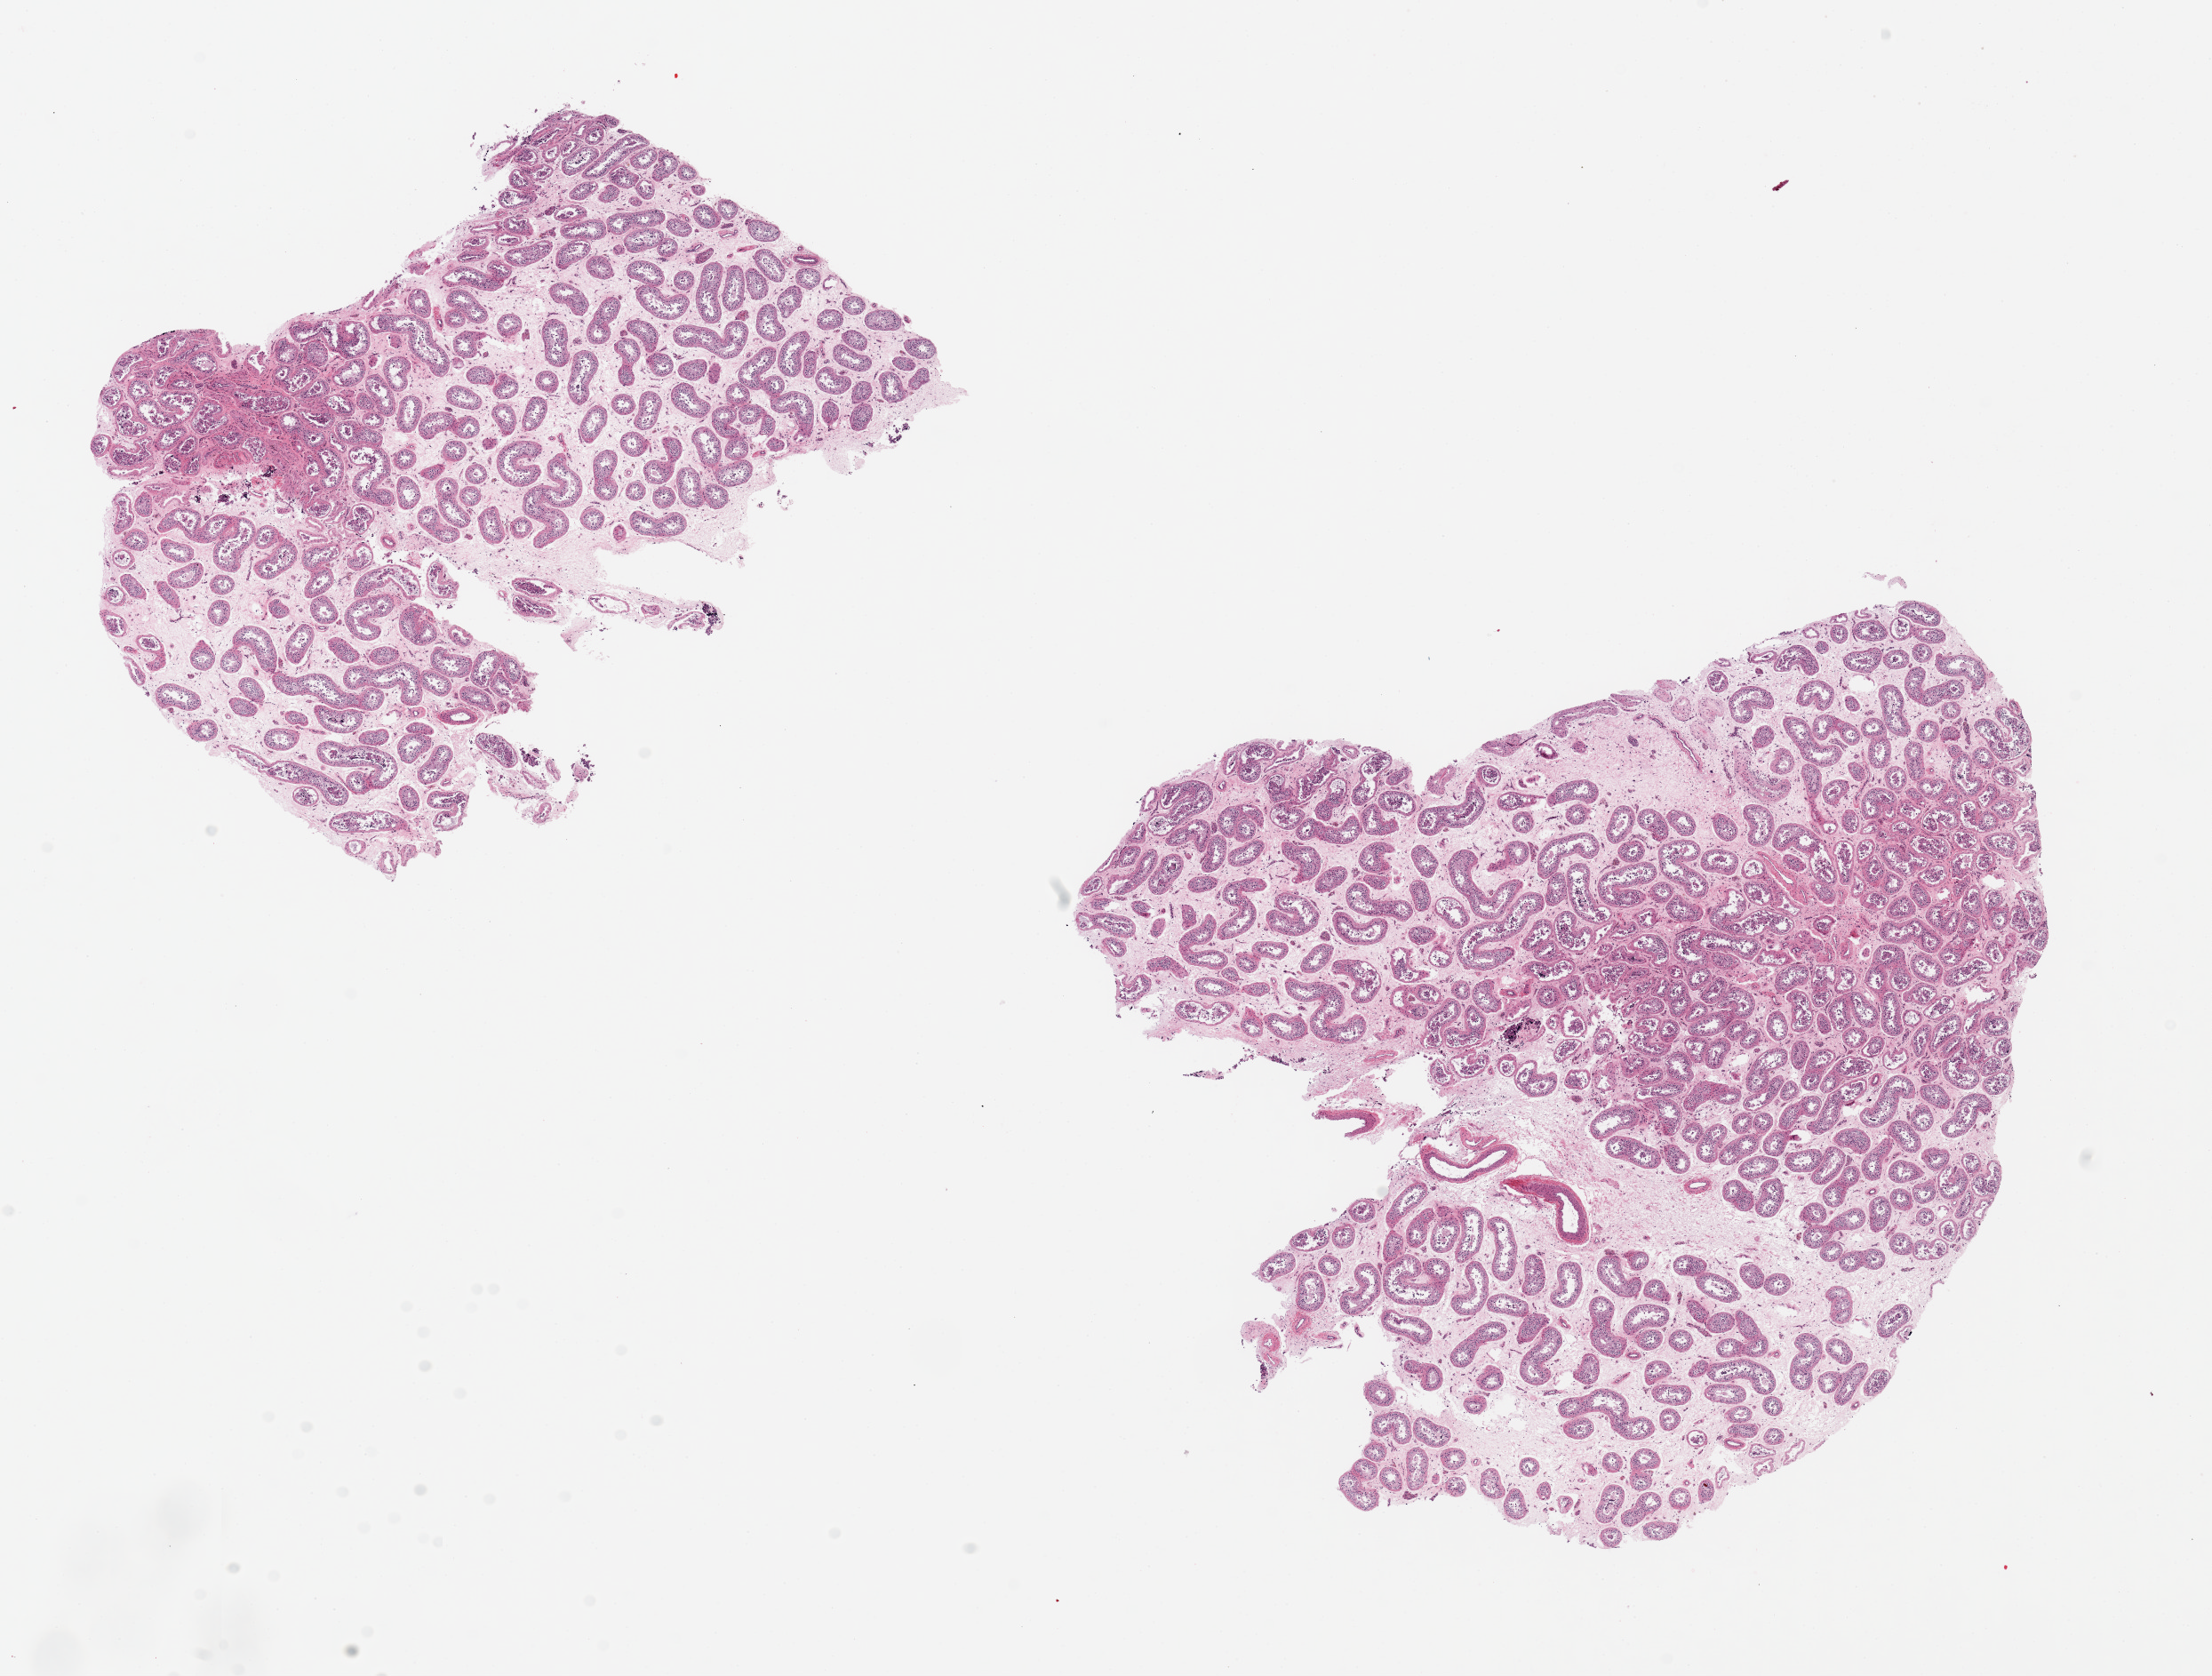
Digitized hematoxylin and eosin (H&E)-stained section — low-resolution overview of the scanned area, about 19.7 x 14.9 mm (slide scanned at 20x); PAXgene-fixed paraffin-embedded (PFPE) section; target tissue: testis; donor tissue sample. Male donor.
Pathologist's review note for this sample: 2 pieces ~9x6mm.